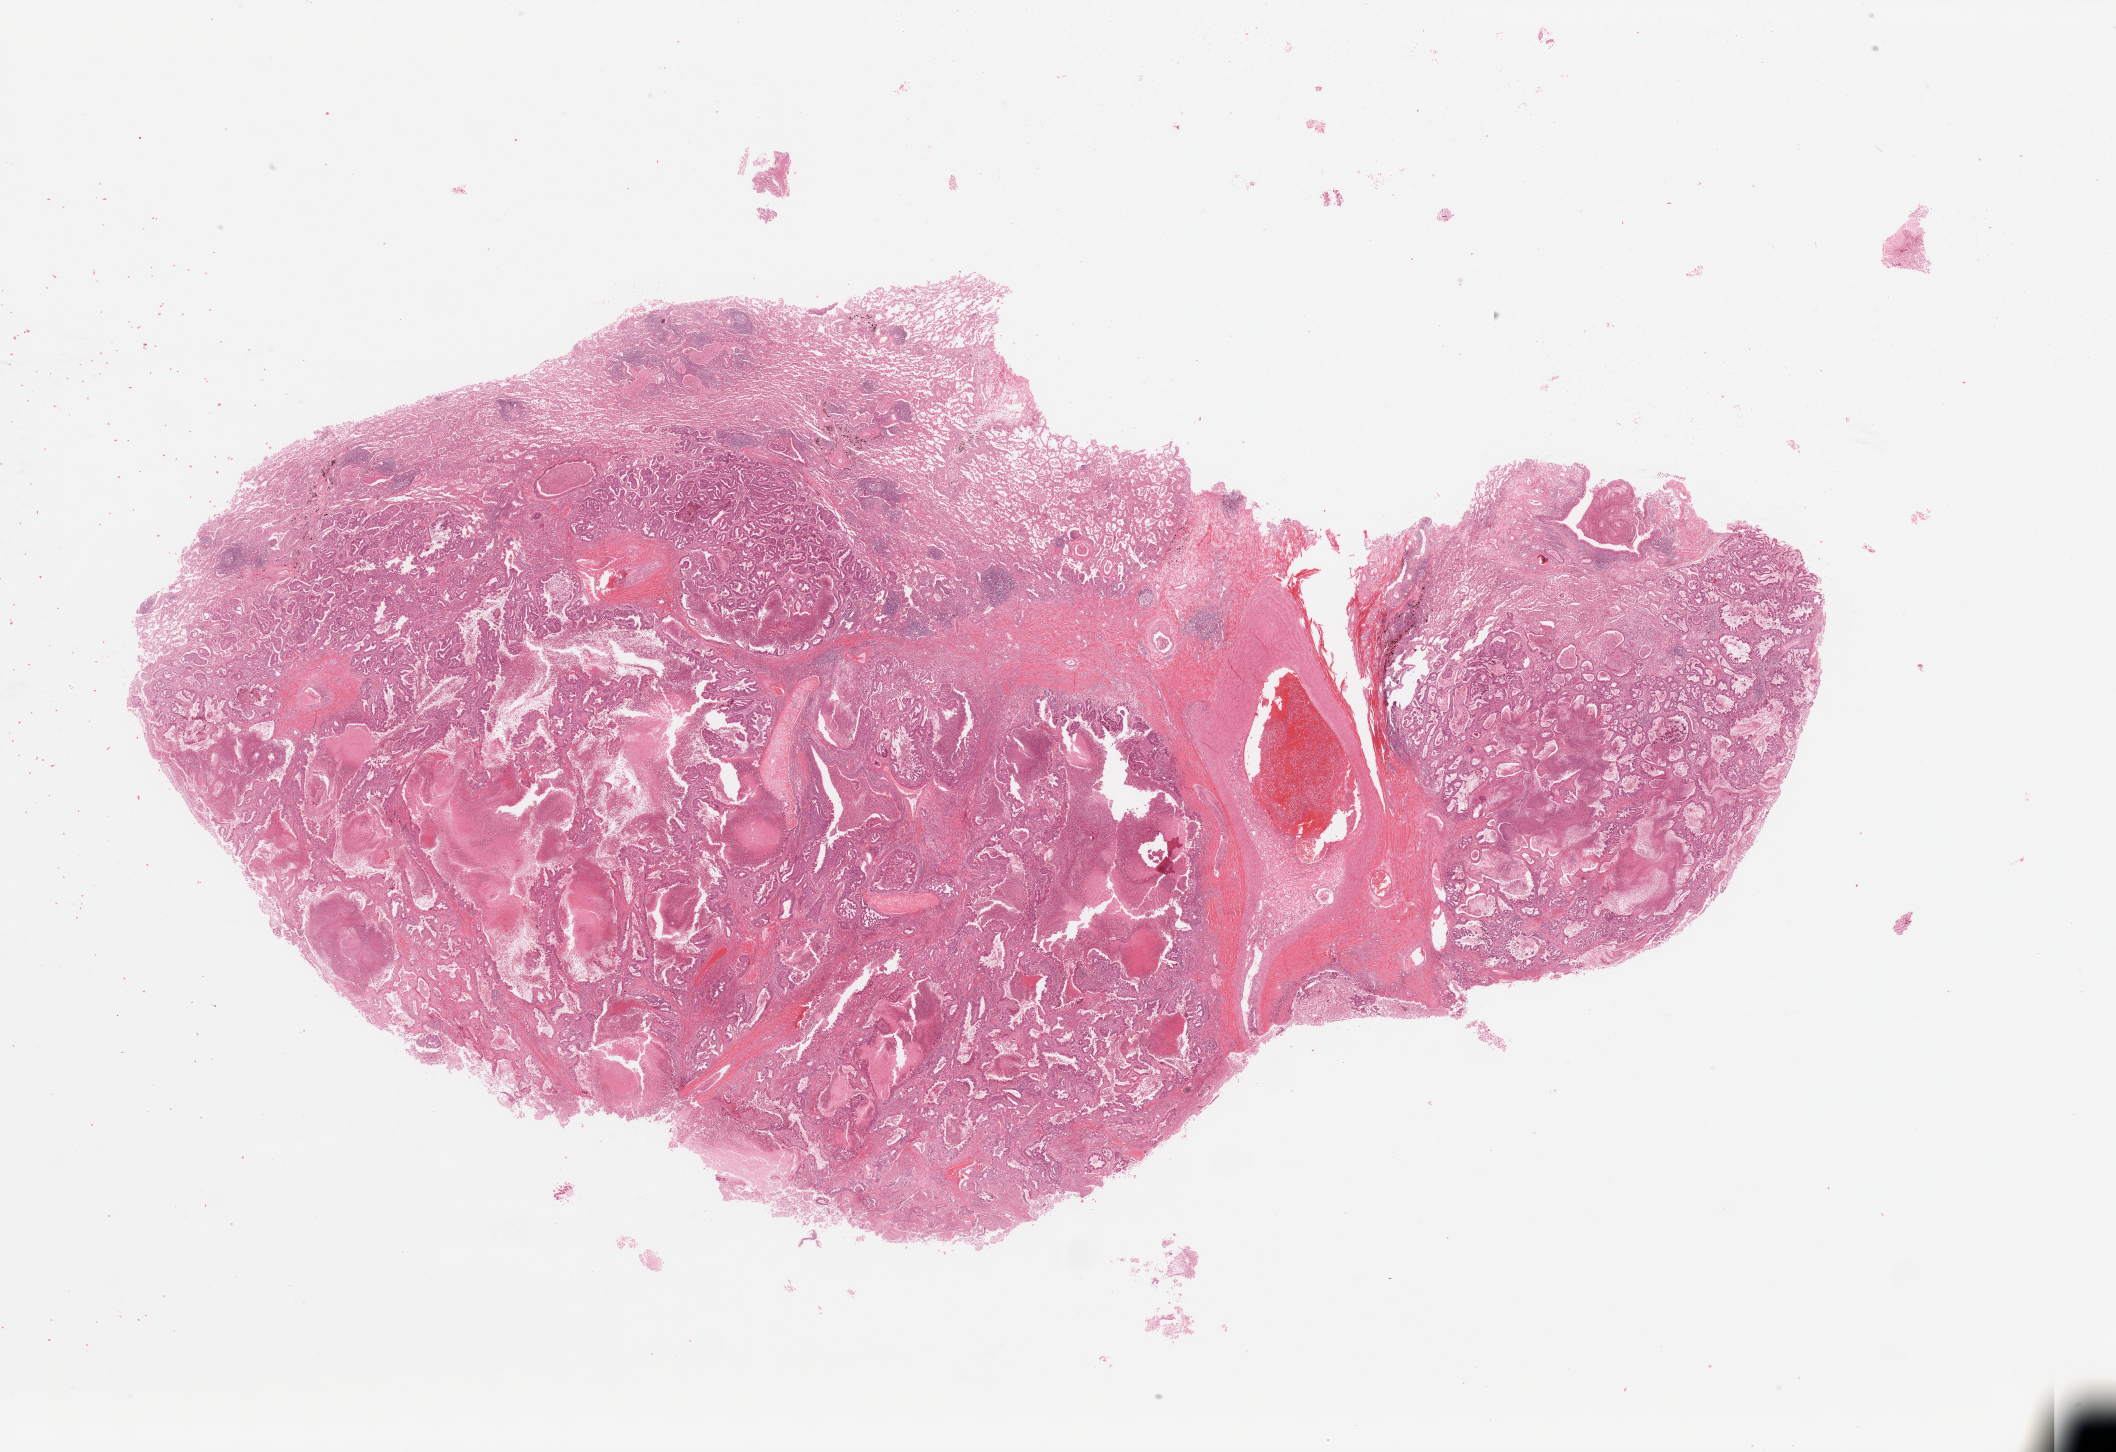
Digitized H&E tissue section (whole slide) — whole scanned area (about 33.5 x 23.0 mm, slide scanned at 20x) shown as a low-resolution overview; lung, tumour tissue. Patient: male, age 49 years. Histologic grade: G2 (moderately differentiated).
* AJCC pathologic stage: IIB
* histologic diagnosis: Adenocarcinoma, NOS